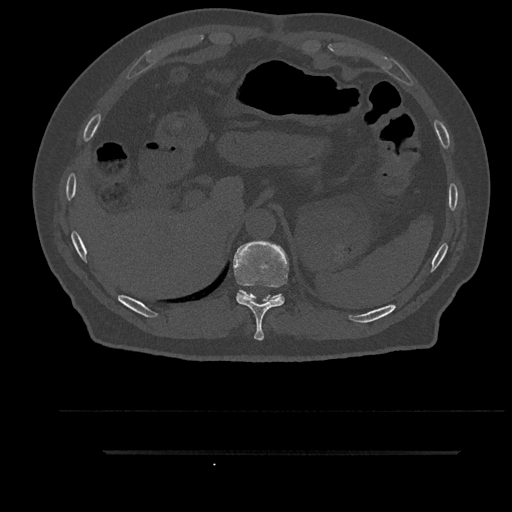
CT including the spine, one axial slice. Slice 348 of 797 in the series (ordered by position). Reconstruction kernel Br40s/3. Bone window (W 1800 / L 400 HU). 0.5 mm slice thickness. 512 × 512 image matrix, field of view 432 × 432 mm. Patient: male, 63 years. Case-level facts recorded for this patient, not image findings: primary cancer: renal.
Outlined on this slice (semi-automatic segmentation, software-assisted and operator-edited):
- T10 vertebra: bounding box [x1, y1, x2, y2] px = [233, 241, 289, 341]
- T11 vertebra: [238, 290, 281, 300]